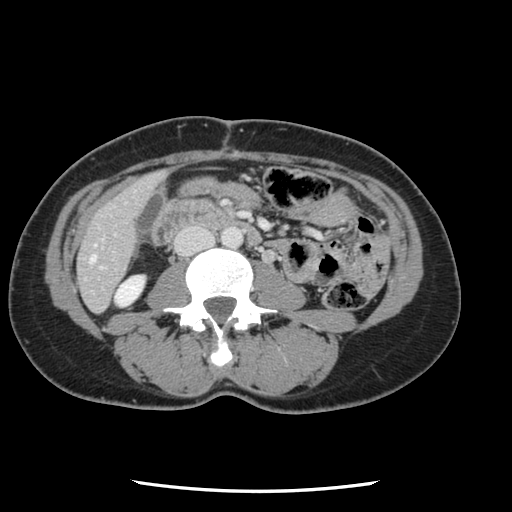
Contrast-enhanced abdominal CT, one axial slice. Position 19 of 134 along the scan axis. Intravenous contrast given. Soft-tissue window (W 400 / L 40 HU). 512 × 512 image matrix, field of view 330 × 330 mm. Female patient, age 43 years. From the clinical record (not read from this slice): diagnosis: colorectal cancer liver metastases, imaged before liver resection; multiple liver metastases: yes; largest metastasis: 3.4 cm.
Outlined on this slice (manually delineated by an expert):
- hepatic veins: bounding box (x1, y1, x2, y2) in pixels: (90, 255, 95, 263)
- liver: (79, 174, 163, 311)
- planned liver remnant (the part of the liver to remain after resection): (79, 174, 162, 311)